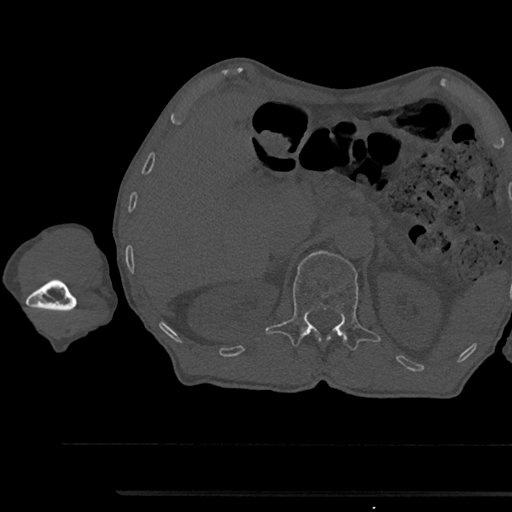
CT including the spine, one axial slice. Slice 654 of 797 in the series (ordered by position). Bone window (W 1800 / L 400 HU). 512 × 512 image matrix, field of view 367 × 367 mm. Patient: male, 79 years. Case-level facts recorded for this patient, not image findings: primary cancer: prostate.
Annotated regions visible in this slice (semi-automatic segmentation, software-assisted and operator-edited):
- L1 vertebra: box from (x=265, y=251) to (x=381, y=350) px